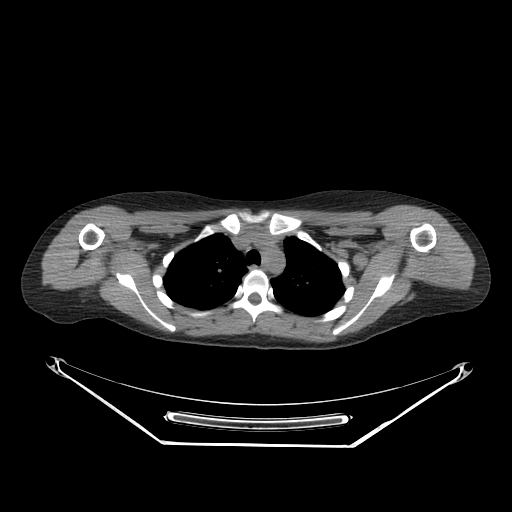
CT of an extremity soft-tissue mass (from a PET/CT study), one axial slice. Position 207 of 267 along the scan axis. 140 kVp. Soft-tissue window (W 400 / L 40 HU). 3.75 mm slice thickness. 512 × 512 image matrix, field of view 500 × 500 mm. Female patient. From the clinical record (not read from this slice): histological type: malignant fibrous histiocytoma; grade: low; site of the primary tumour: left arm.
Structures marked on this image (expert contour drawn on MRI and transferred to this co-registered scan by the dataset authors):
- gross tumour volume (mass): box from (x=420, y=249) to (x=458, y=284) px